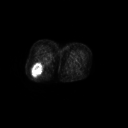
FDG PET of an extremity soft-tissue mass (from a PET/CT study), one axial slice. 3.27 mm slice thickness. 128 × 128 image matrix, field of view 700 × 700 mm. Female patient, age 70 years. From the clinical record (not read from this slice): histological type: synovial sarcoma; grade: intermediate; site of the primary tumour: right buttock.
Annotated regions visible in this slice (expert contour drawn on MRI and transferred to this co-registered scan by the dataset authors):
- gross tumour volume including surrounding oedema: box from (x=31, y=61) to (x=42, y=75) px
- gross tumour volume (mass): (x=32, y=62)–(x=42, y=74)